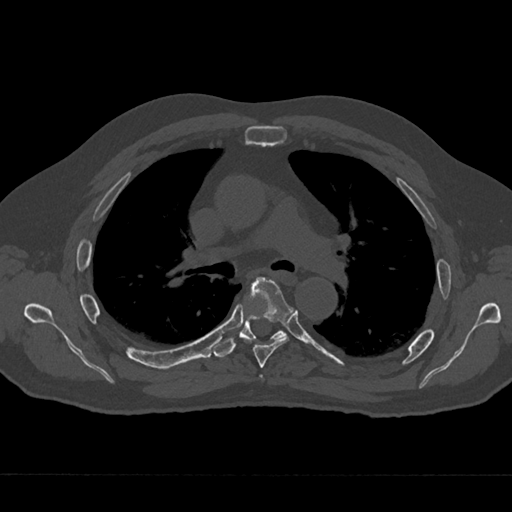
CT including the spine, one axial slice. Reconstruction kernel Br40s/3. 120 kVp. Bone window (W 1800 / L 400 HU). 0.5 mm slice thickness. 512 × 512 image matrix, field of view 377 × 377 mm. Male patient, age 75 years. Case-level facts recorded for this patient, not image findings: primary cancer: renal.
Annotated regions visible in this slice (semi-automatic segmentation, software-assisted and operator-edited):
- T4 vertebra: bounding box <260,375,263,378> (left, top, right, bottom; pixels)
- T5 vertebra: <245,277,293,368>
- T6 vertebra: <214,278,287,358>